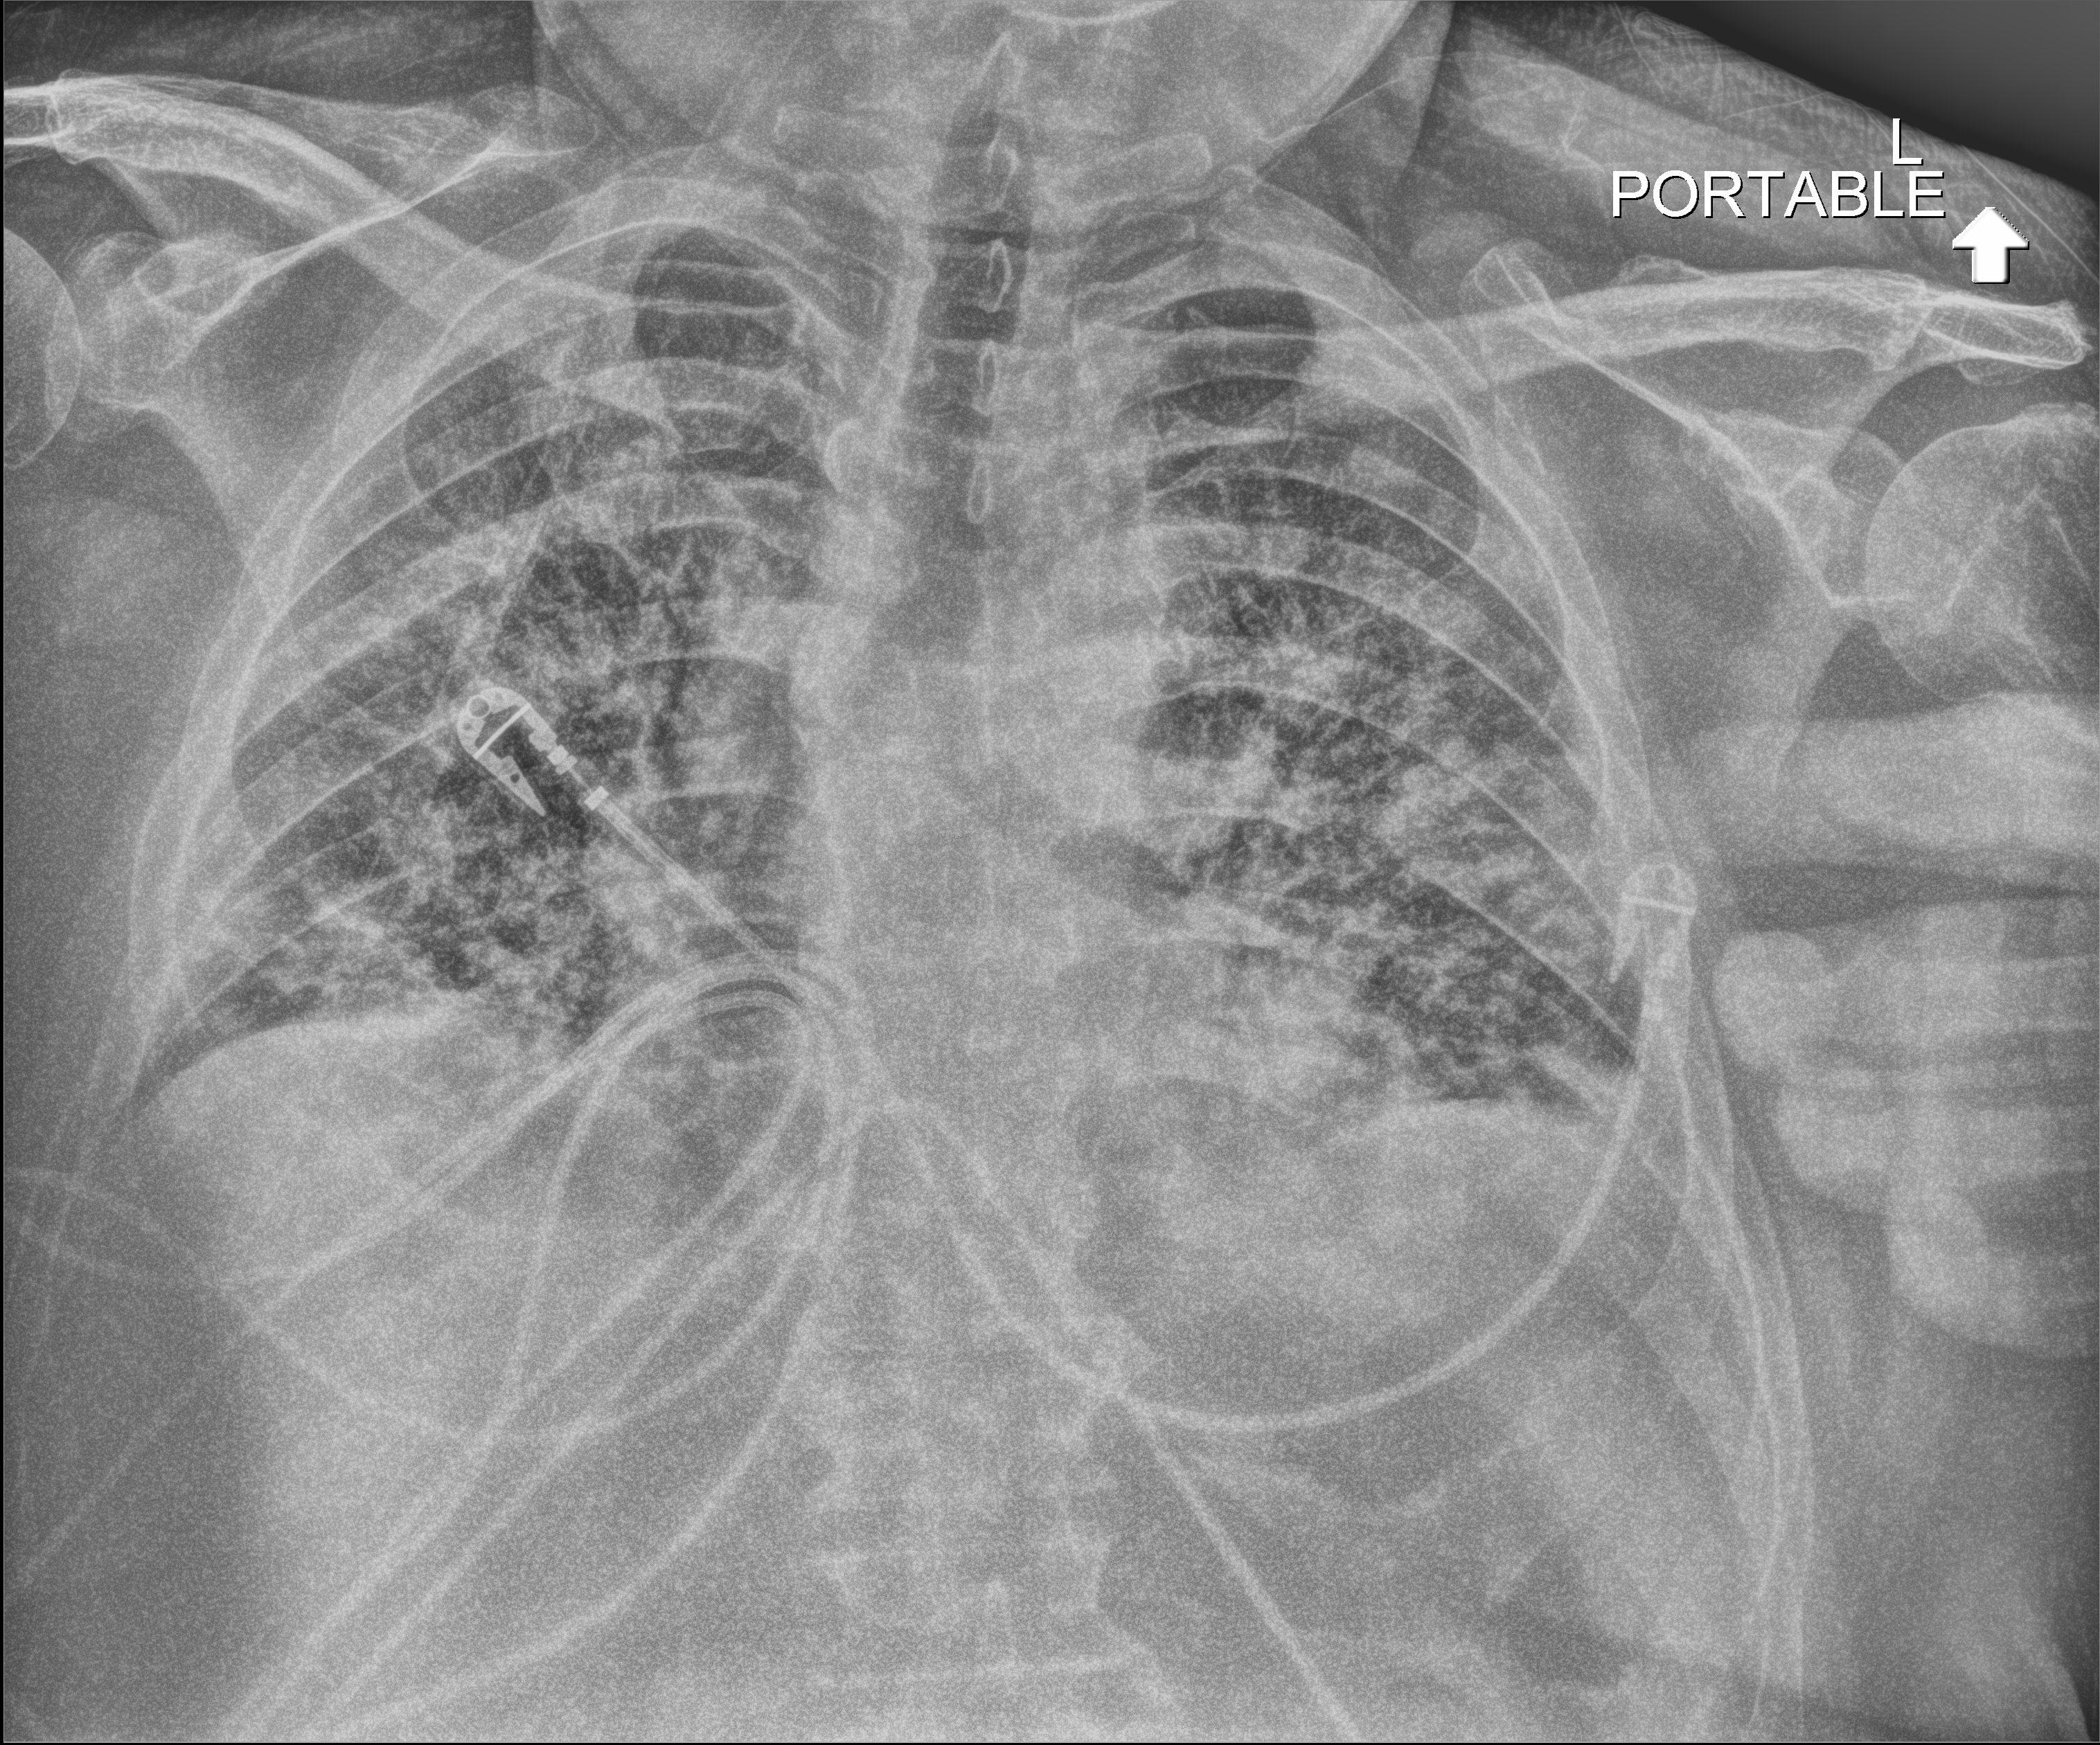
Chest radiograph (digital radiography); anteroposterior (AP) projection. Male patient hospitalised with COVID-19, age 18–59 years.
From the hospital-stay record, not from the radiograph (when in the stay this image was taken is not recorded): admitted to intensive care during this hospital stay: no; chronic kidney disease (admission record): no.